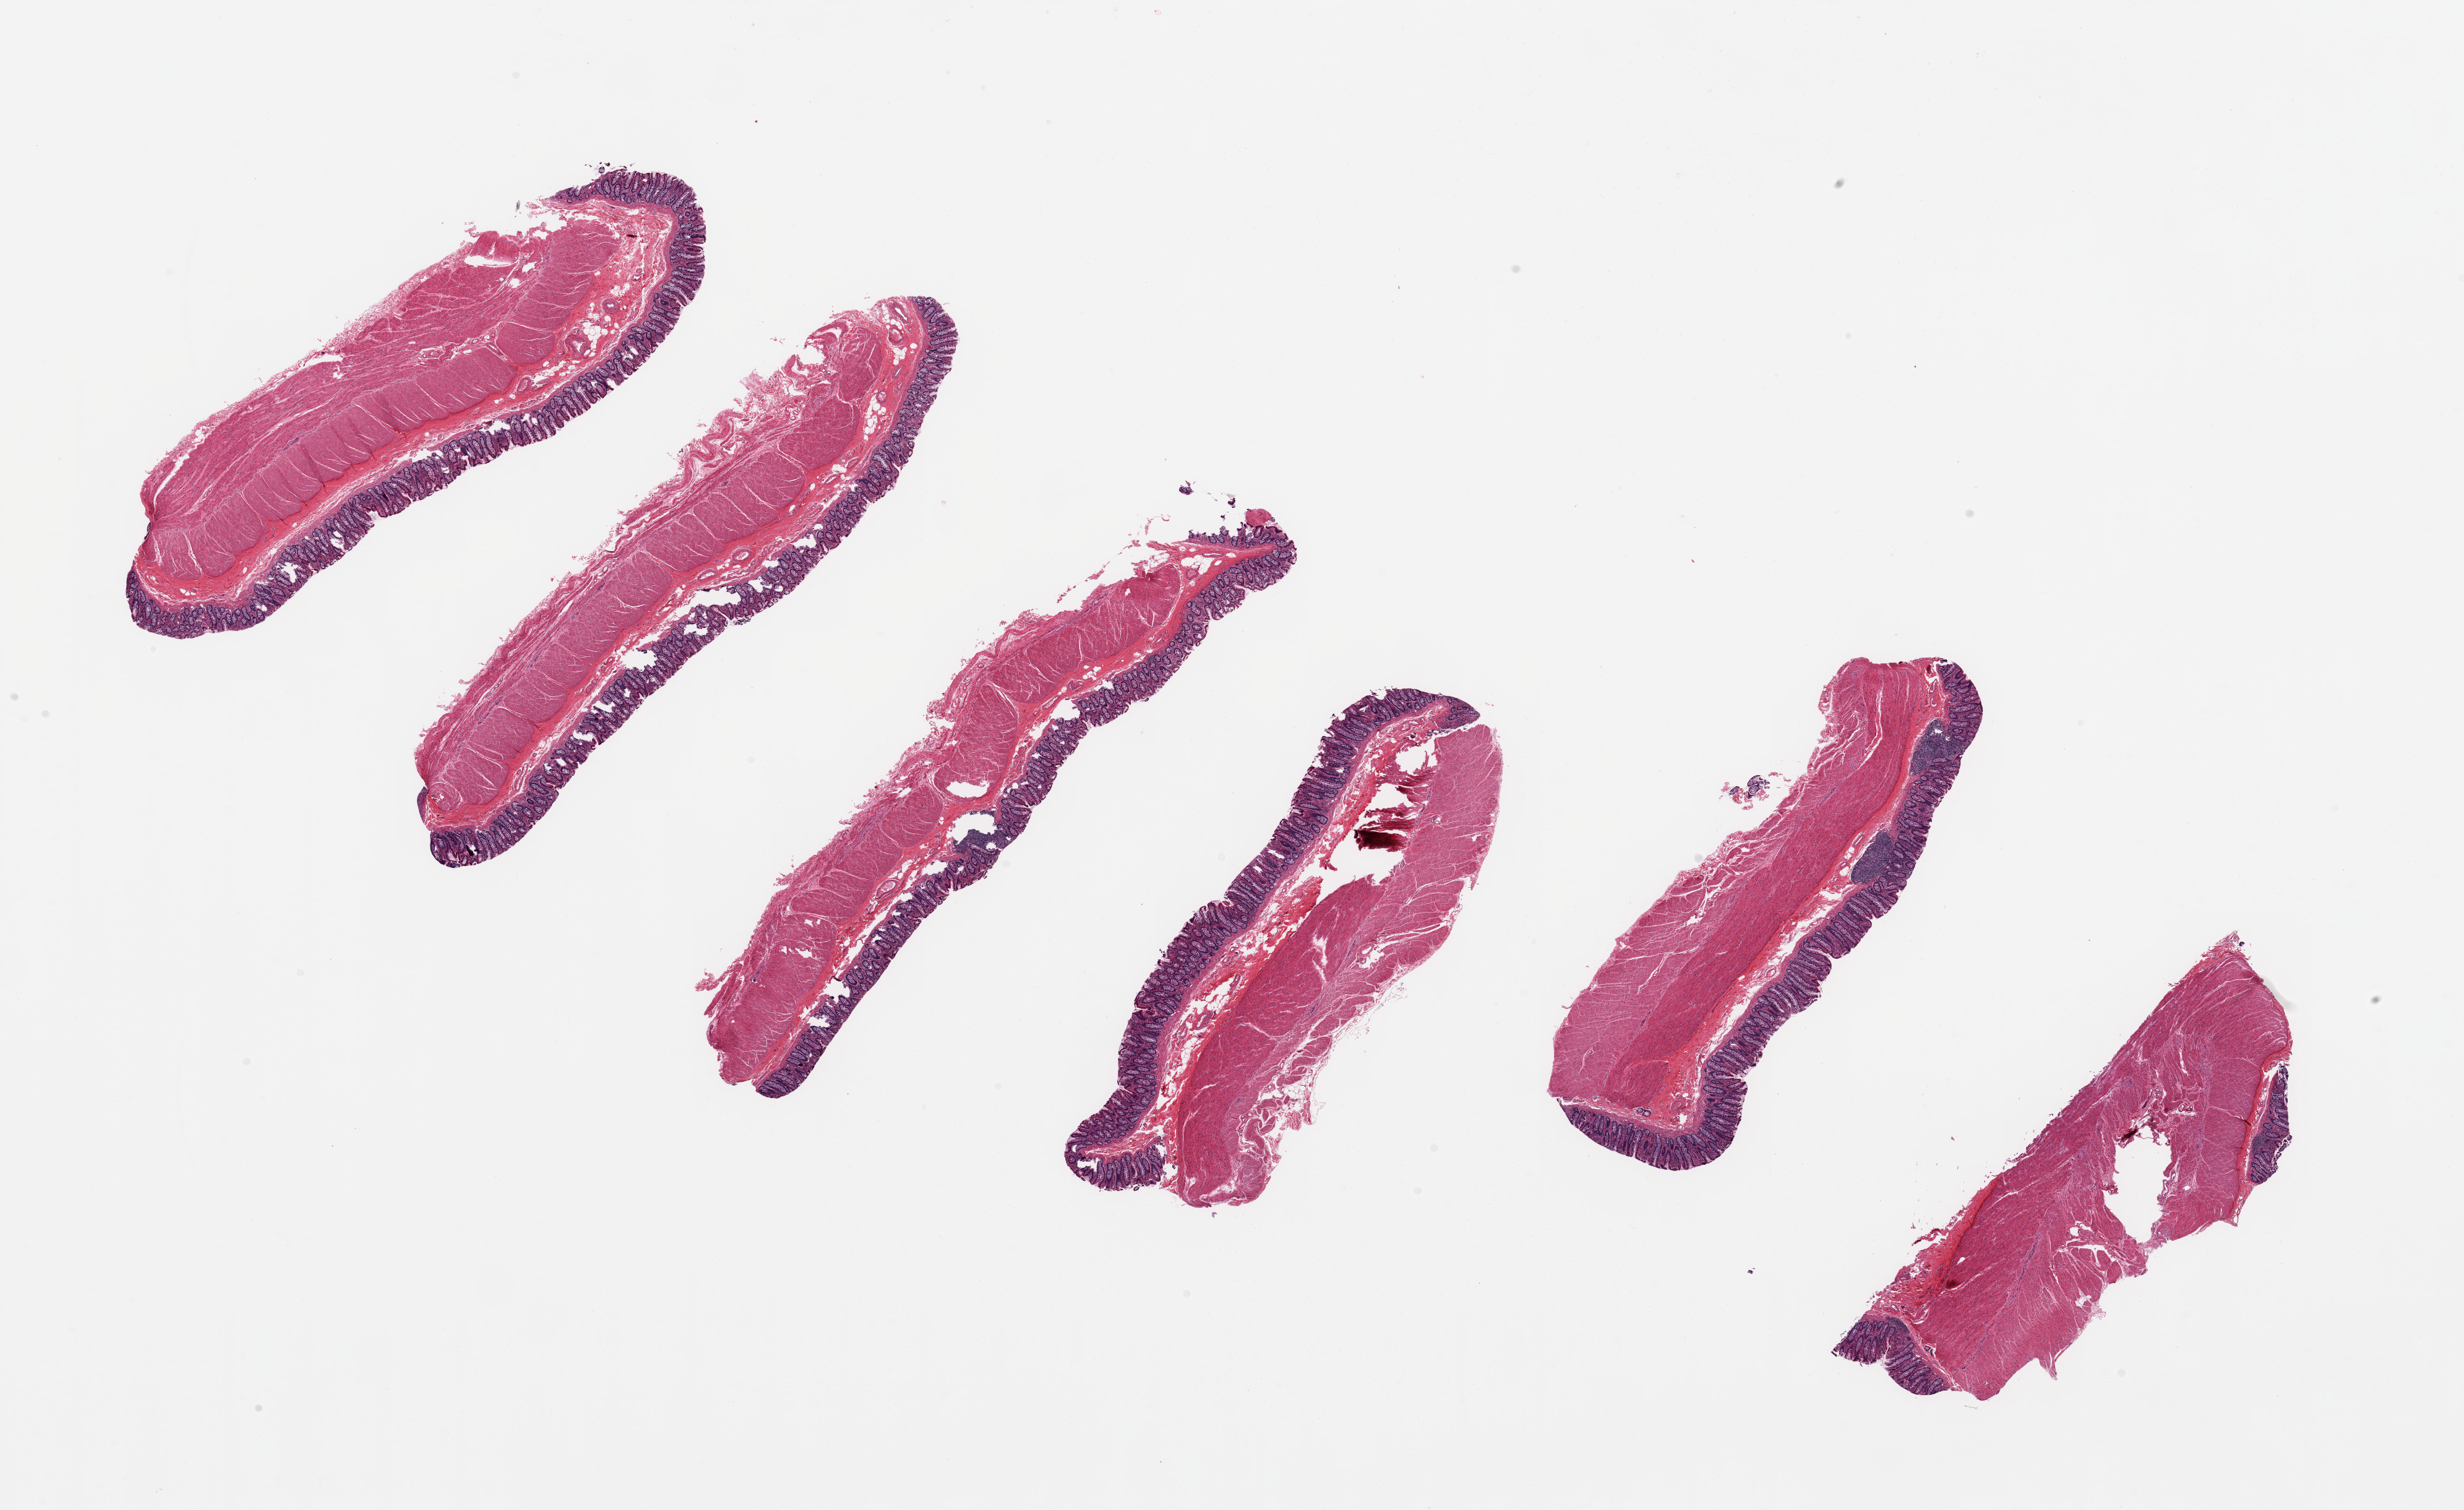
Haematoxylin and eosin whole-slide image, brightfield, a low-resolution overview of the entire scanned area, about 31.5 x 19.3 mm (acquisition: 20x scan). PAXgene-fixed, paraffin-embedded tissue. Target tissue: transverse colon. Donor tissue sample. Female donor.
Reviewer comment on this tissue sample: 6 well-preserved pieces, ~7x2mm. Mucosa is ~20-25% thickness. Areas of under-fixation with tears.